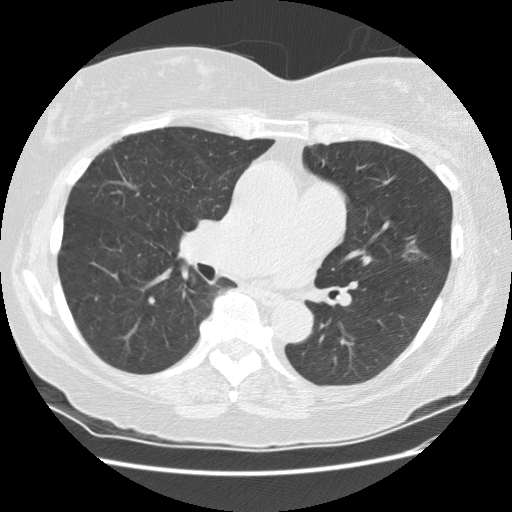
Chest CT (low-dose screening protocol), one axial image, second screening round (one year after baseline), lung window (W 1500 / L -600 HU), 512 × 512 image matrix, field of view 360 × 360 mm. Female participant, aged 71 years at enrolment. Former smoker at enrolment.
- Expert-annotated lung lesion, bounding box (x1, y1, x2, y2) in pixels: (385, 226, 437, 271).
- Screening reader's record for this exam (one nodule recorded; not confirmed to be the boxed lesion): non-calcified nodule or mass ≥4 mm, lingula, 13 × 13 mm, poorly defined margins, ground glass attenuation, pre-existing on the prior screen: yes; interval growth: yes.
- Official screen result: positive, change unspecified: nodule(s) >= 4 mm or enlarging nodule(s), mass(es), or other non-specific abnormalities suspicious for lung cancer.
- Participant outcome: lung cancer diagnosed 26 days after this screen — adenocarcinoma, NOS, left upper lobe, well differentiated (G1), stage IA (AJCC 6th edition), 11 mm at pathology.